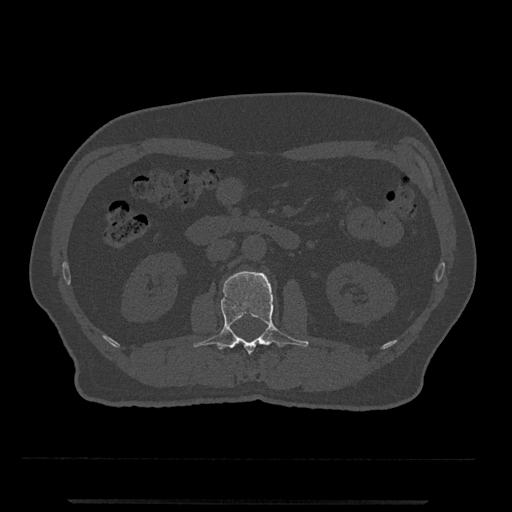
CT including the spine, one axial slice. Slice 270 of 797 in the series (ordered by position). Reconstruction kernel Br40s/3. 120 kVp. Bone window (W 1800 / L 400 HU). 0.5 mm slice thickness. 512 × 512 image matrix, field of view 419 × 419 mm. Patient: male, 63 years. Case-level facts recorded for this patient, not image findings: primary cancer: prostate.
Structures marked on this image (semi-automatically segmented with operator editing):
- L2 vertebra: bounding box <193,271,309,354> (left, top, right, bottom; pixels)